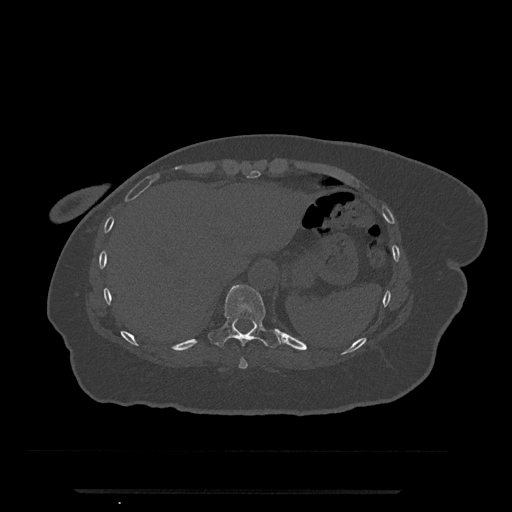
CT including the spine, one axial slice. Slice 294 of 797 in the series (ordered by position). Reconstruction kernel Br40s/3. Bone window (W 1800 / L 400 HU). 0.5 mm slice thickness. 512 × 512 image matrix, field of view 440 × 440 mm. Patient: female, 51 years. Case-level facts recorded for this patient, not image findings: primary cancer: neuro; vertebrae with lytic lesions (as recorded): T8.
Structures marked on this image (semi-automatic segmentation, software-assisted and operator-edited):
- T10 vertebra: bounding box [x1, y1, x2, y2] px = [210, 285, 281, 348]
- T9 vertebra: [239, 357, 248, 369]